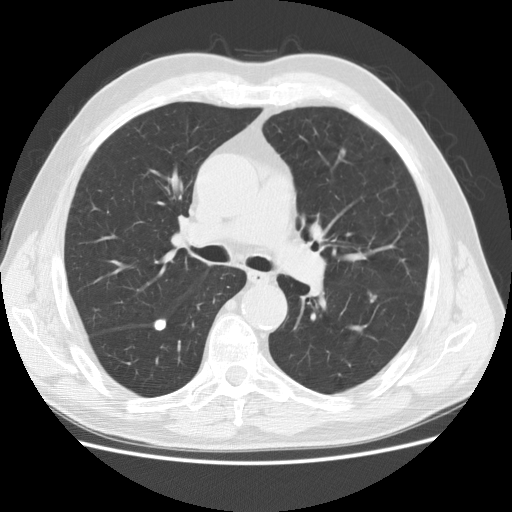
Axial slice from a low-dose chest CT screening exam. First (baseline) screen. Lung window (W 1500 / L -600 HU). 120 kVp. Slice 65 of 155 in the series. Male participant, aged 73 years at enrolment.
Expert reader's lesion annotation, box from (x=351, y=281) to (x=392, y=310) px. No non-calcified nodule or mass ≥4 mm was recorded by the screening reader at this exam. Official screen result: negative screen, significant abnormalities not suspicious for lung cancer. Participant outcome: lung cancer diagnosed 536 days after this screen — adenocarcinoma, NOS, left lower lobe, poorly differentiated (G3), stage IIA (AJCC 6th edition), 12 mm at pathology.